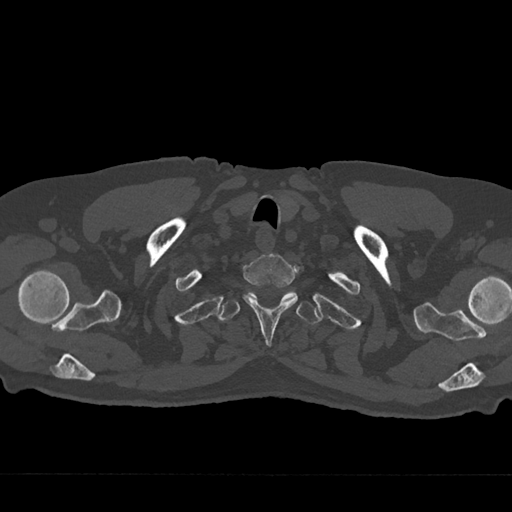
CT including the spine, one axial slice; position 643 of 797 along the scan axis; reconstruction kernel Br40s/3; 120 kVp; bone window (W 1800 / L 400 HU); 0.5 mm slice thickness; 512 × 512 image matrix, field of view 377 × 377 mm. Male patient, age 75 years. From the clinical record (not read from this slice): primary cancer: renal.
Structures marked on this image (semi-automatically segmented with operator editing):
- T1 vertebra: bounding box (x1, y1, x2, y2) in pixels: (243, 254, 298, 346)
- T2 vertebra: (218, 290, 321, 324)